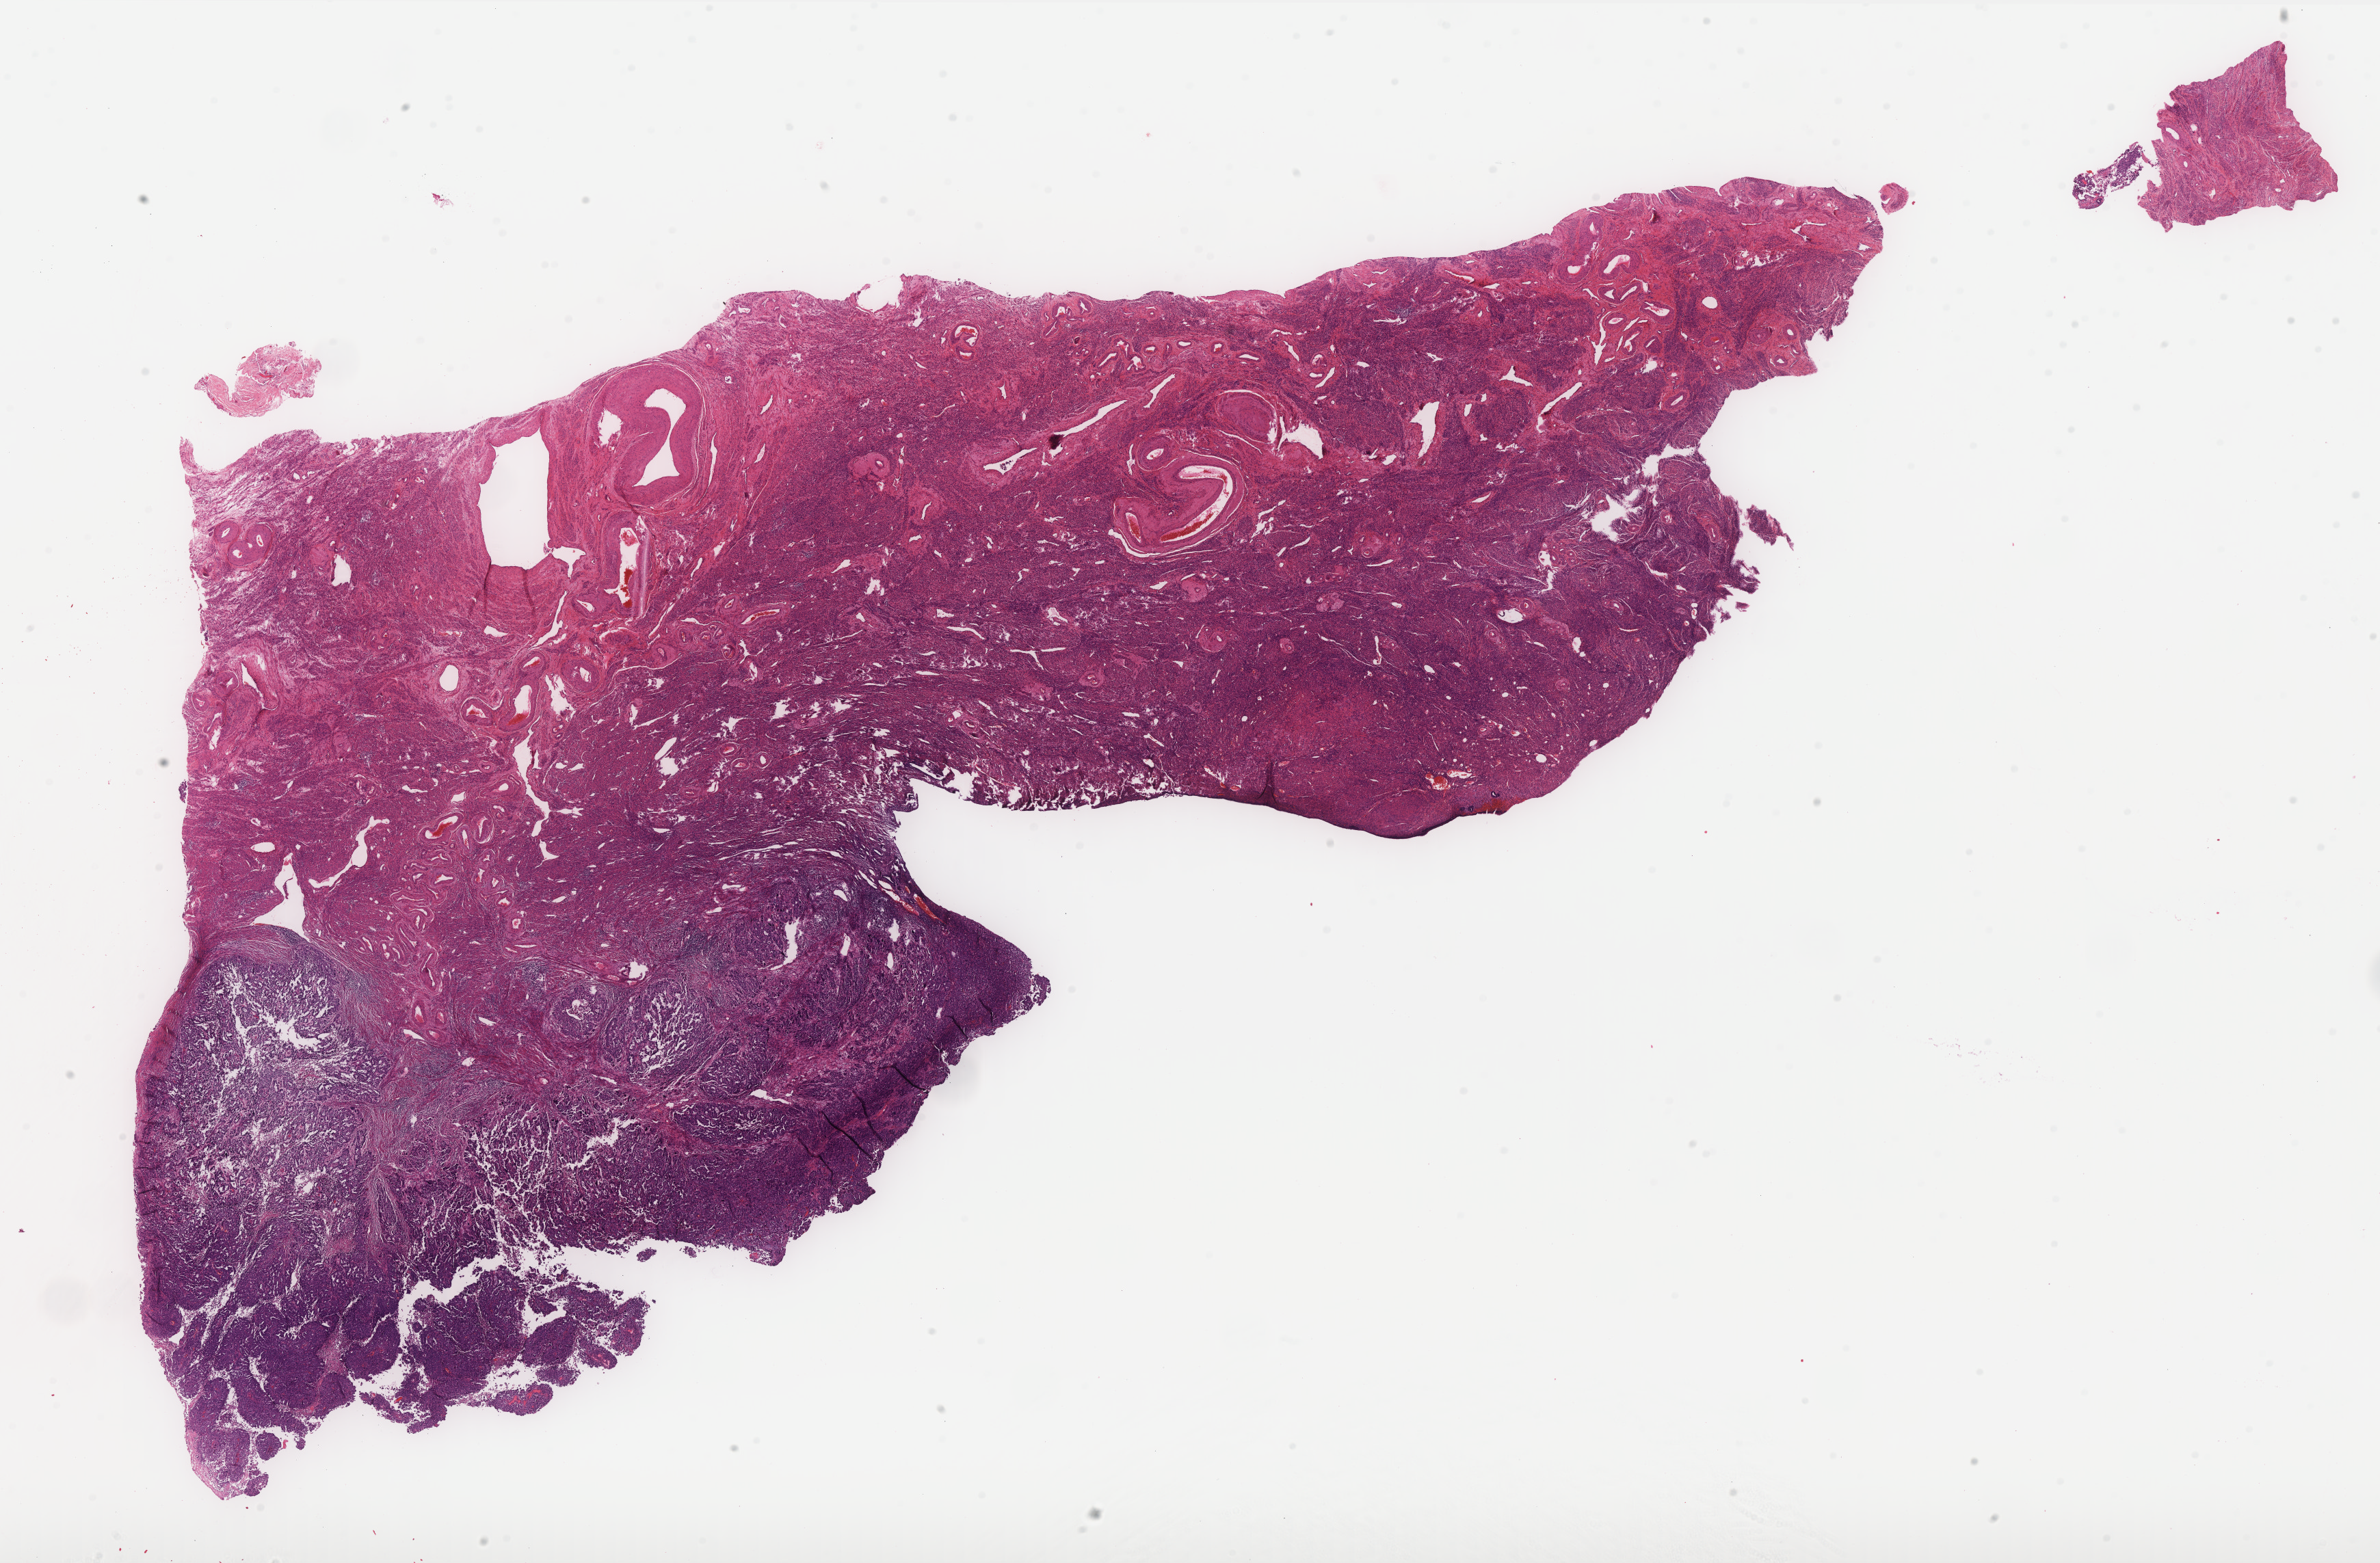
Whole-slide histology image, Hematoxylin and eosin (H&E) stained — whole scanned area (about 27.9 x 18.3 mm) shown as a low-resolution overview; formalin-fixed paraffin-embedded (FFPE) diagnostic section; sample: primary tumour, uterus. Patient: female, age at initial diagnosis 57 years. Histologic grade: G3 (poorly differentiated).
Diagnosis: Serous cystadenocarcinoma, NOS (endometrium). FIGO stage: IIIB.